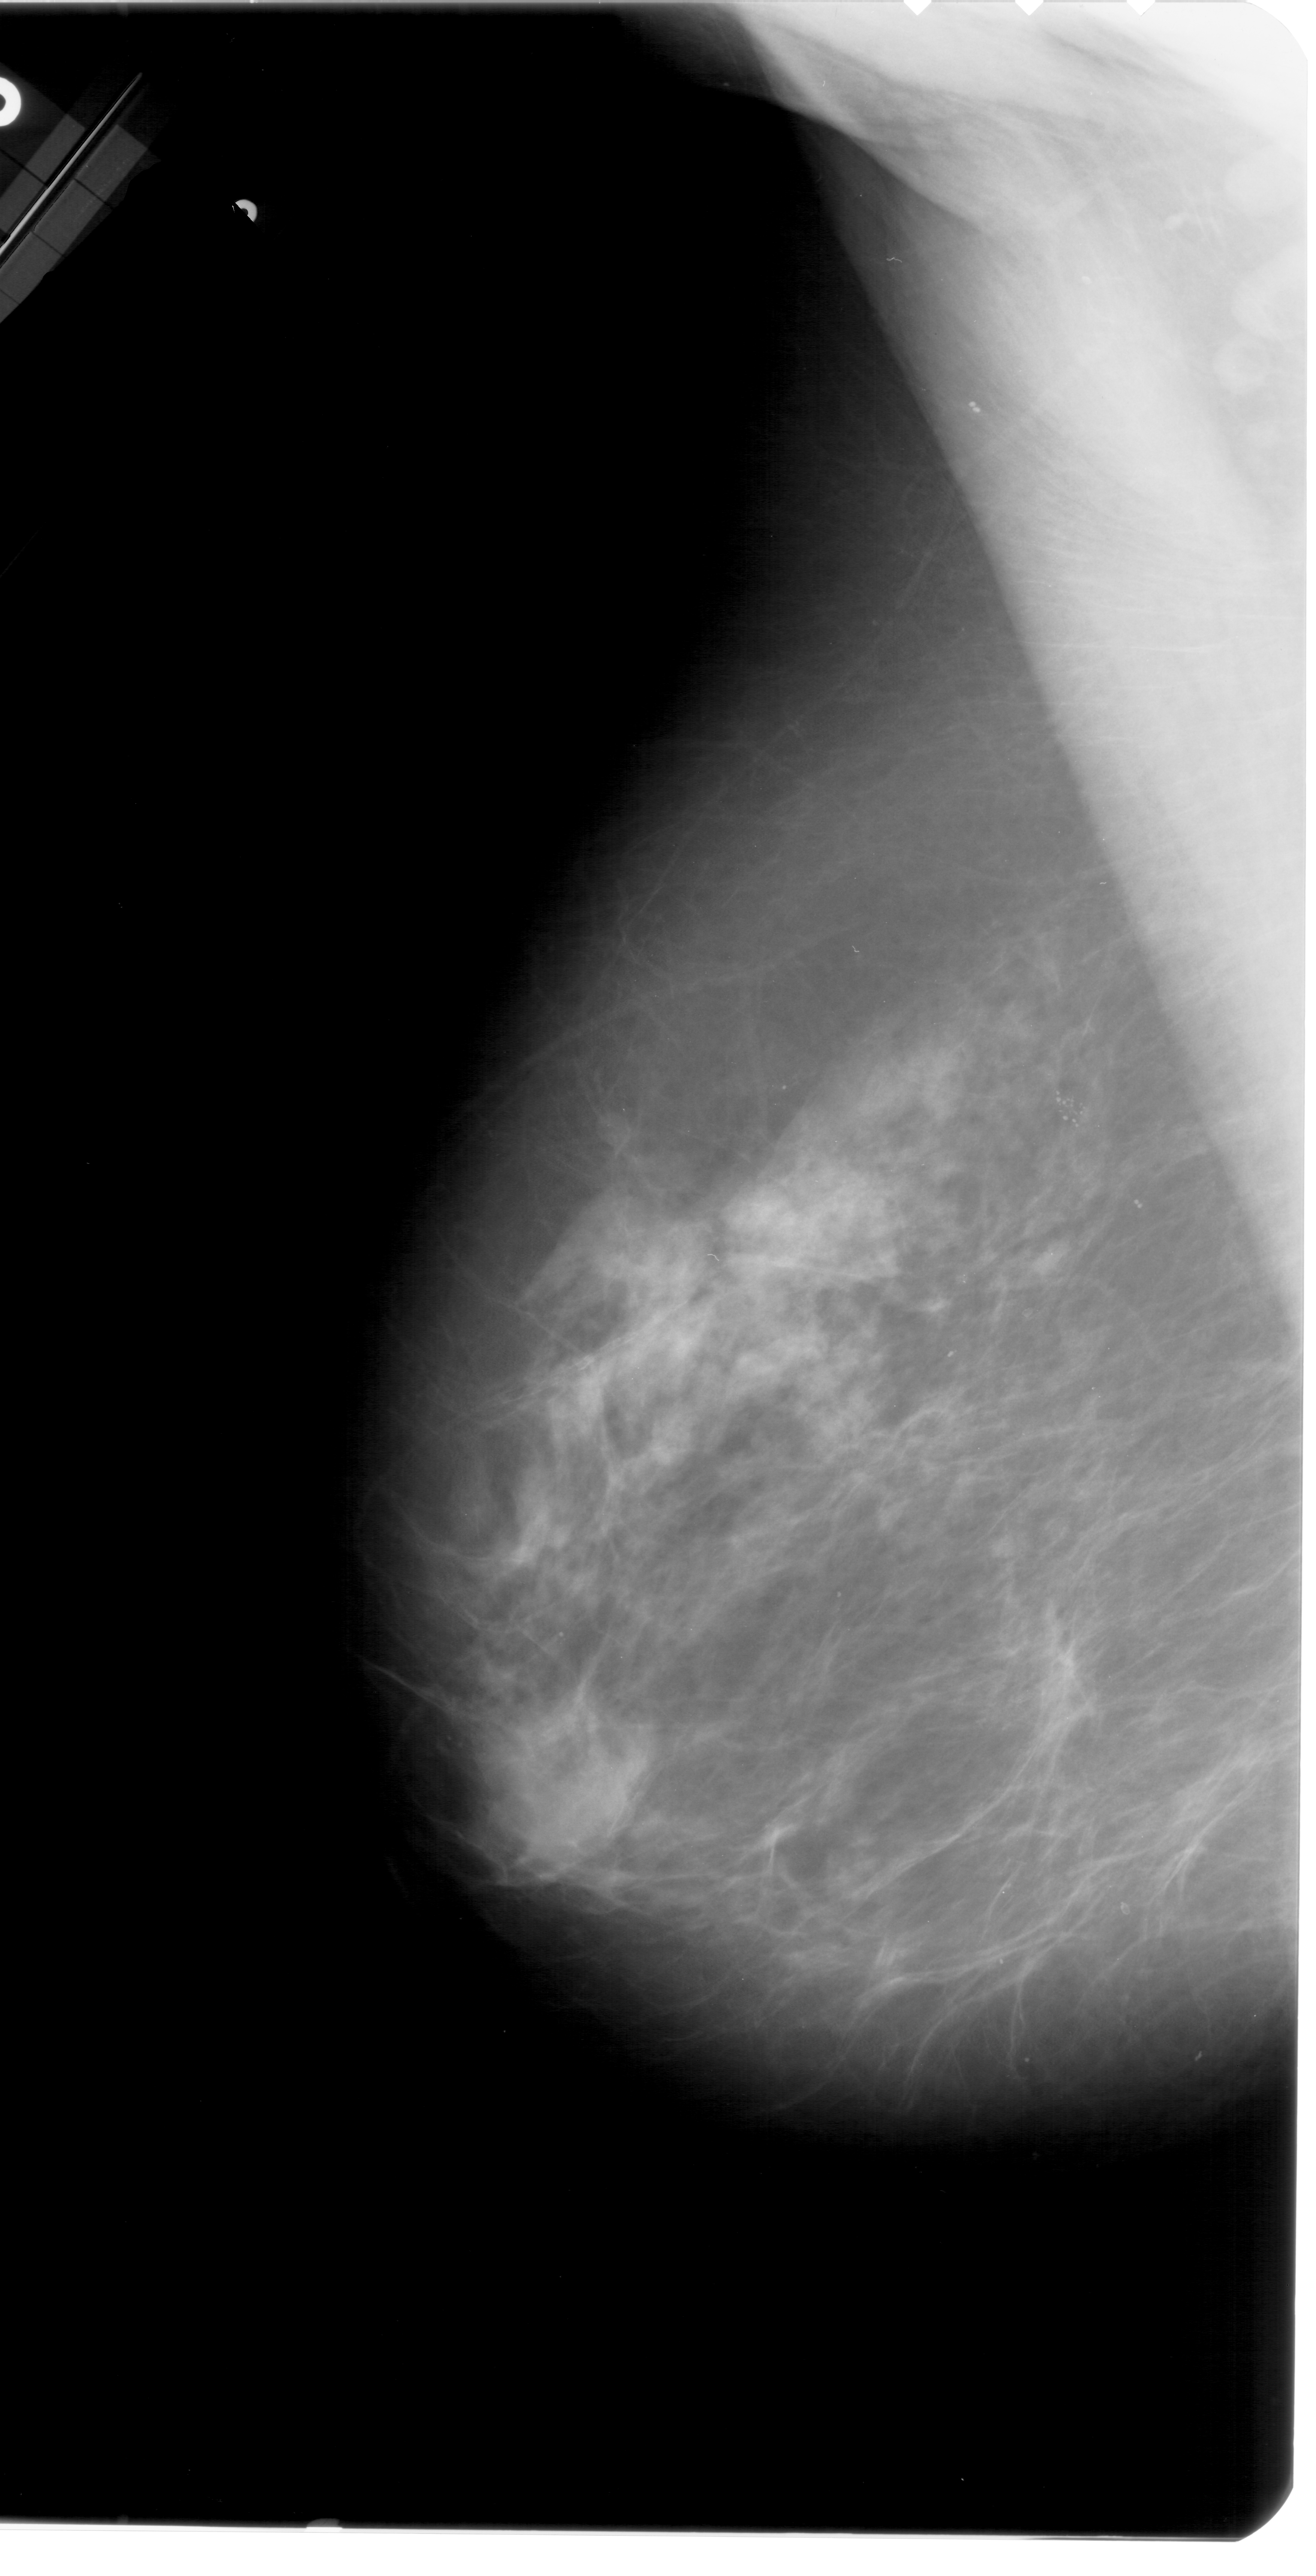
Scanned film-screen mammogram, left breast, mediolateral oblique (MLO) view, BI-RADS breast density category 3 (scale 1–4).
Finding: calcifications, morphology pleomorphic, distribution clustered; BI-RADS assessment category 4; subtlety rating 4 on a 1 (subtle) to 5 (obvious) scale; pathology result (as recorded, not read from the image): malignant.